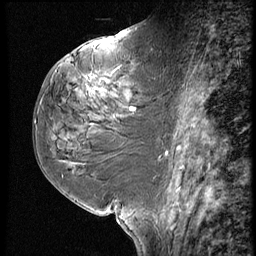
Breast MRI (dynamic contrast-enhanced), one sagittal slice. Position 33 of 60 along the scan axis. 3 images stored at this slice position (order not interpretable as contrast timing). 1.5 T. TE 4.2 ms, TR 9 ms. 2.5 mm slice thickness. 256 × 256 image matrix, field of view 180 × 180 mm. Female patient, age 59 years. Case-level facts recorded for this patient, not image findings: setting: breast cancer imaged before/during neoadjuvant chemotherapy; receptor status: HER2-positive.
Structures marked on this image (semi-automatically segmented with operator editing):
- analysis volume of interest (the breast-tissue region the enhancement analysis was run in; not a lesion): box from (x=78, y=61) to (x=161, y=125) px
- tumour enhancement mask (voxels above the 140 % enhancement threshold inside the analysis volume of interest): (x=132, y=109)–(x=136, y=111)